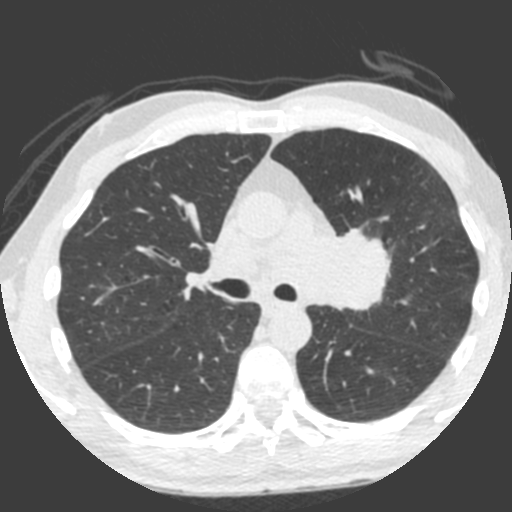
Chest CT (low-dose screening protocol), one axial image. Third annual screen. Lung window (W 1500 / L -600 HU). 2 mm slice thickness. Slice 138 of 212 in the series. Male, age 55 years at enrolment. Current smoker at enrolment.
• Lesion marked by an expert reader, bounding box <309,220,396,324> (left, top, right, bottom; pixels).
• Screening reader's record for this exam (one nodule recorded; not confirmed to be the boxed lesion): non-calcified nodule or mass ≥4 mm, left upper lobe, 49 × 29 mm, spiculated (stellate) margins, soft tissue attenuation, pre-existing on the prior screen: yes; interval growth: yes.
• Official screen result: positive, other.
• Lung cancer was diagnosed 0 days after this screen: small cell carcinoma, NOS, left upper lobe, undifferentiated (G4), stage IV (AJCC 6th edition), 60 mm at pathology.